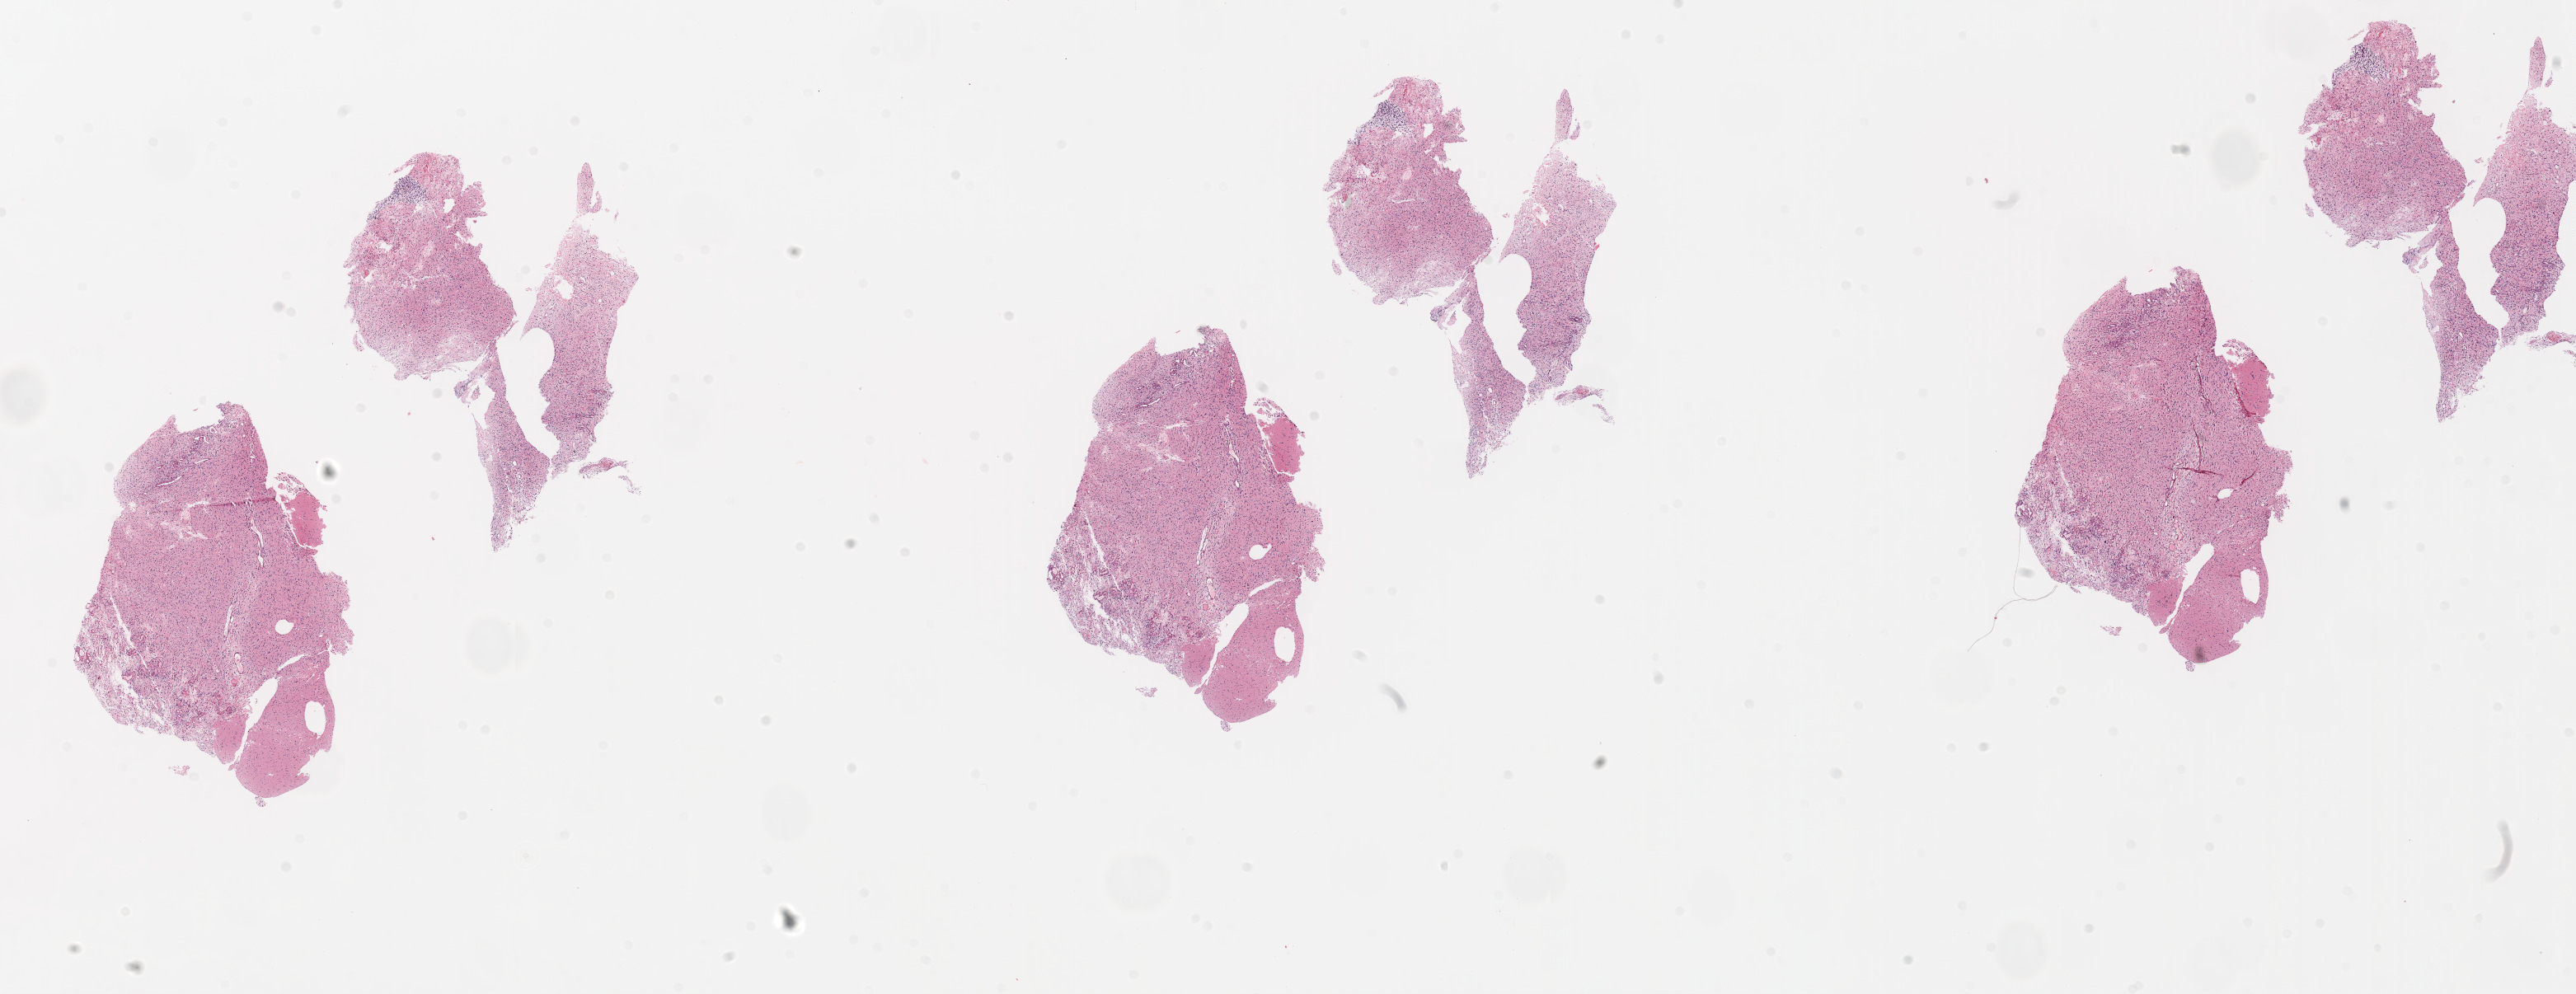
H&E-stained whole-slide image, shown as a low-resolution overview of the whole scanned area (about 25.1 x 9.7 mm); formalin-fixed paraffin-embedded (FFPE) diagnostic section; sample: primary tumour, brain. Female, age 28 years at initial diagnosis.
Histologic diagnosis: Glioblastoma.